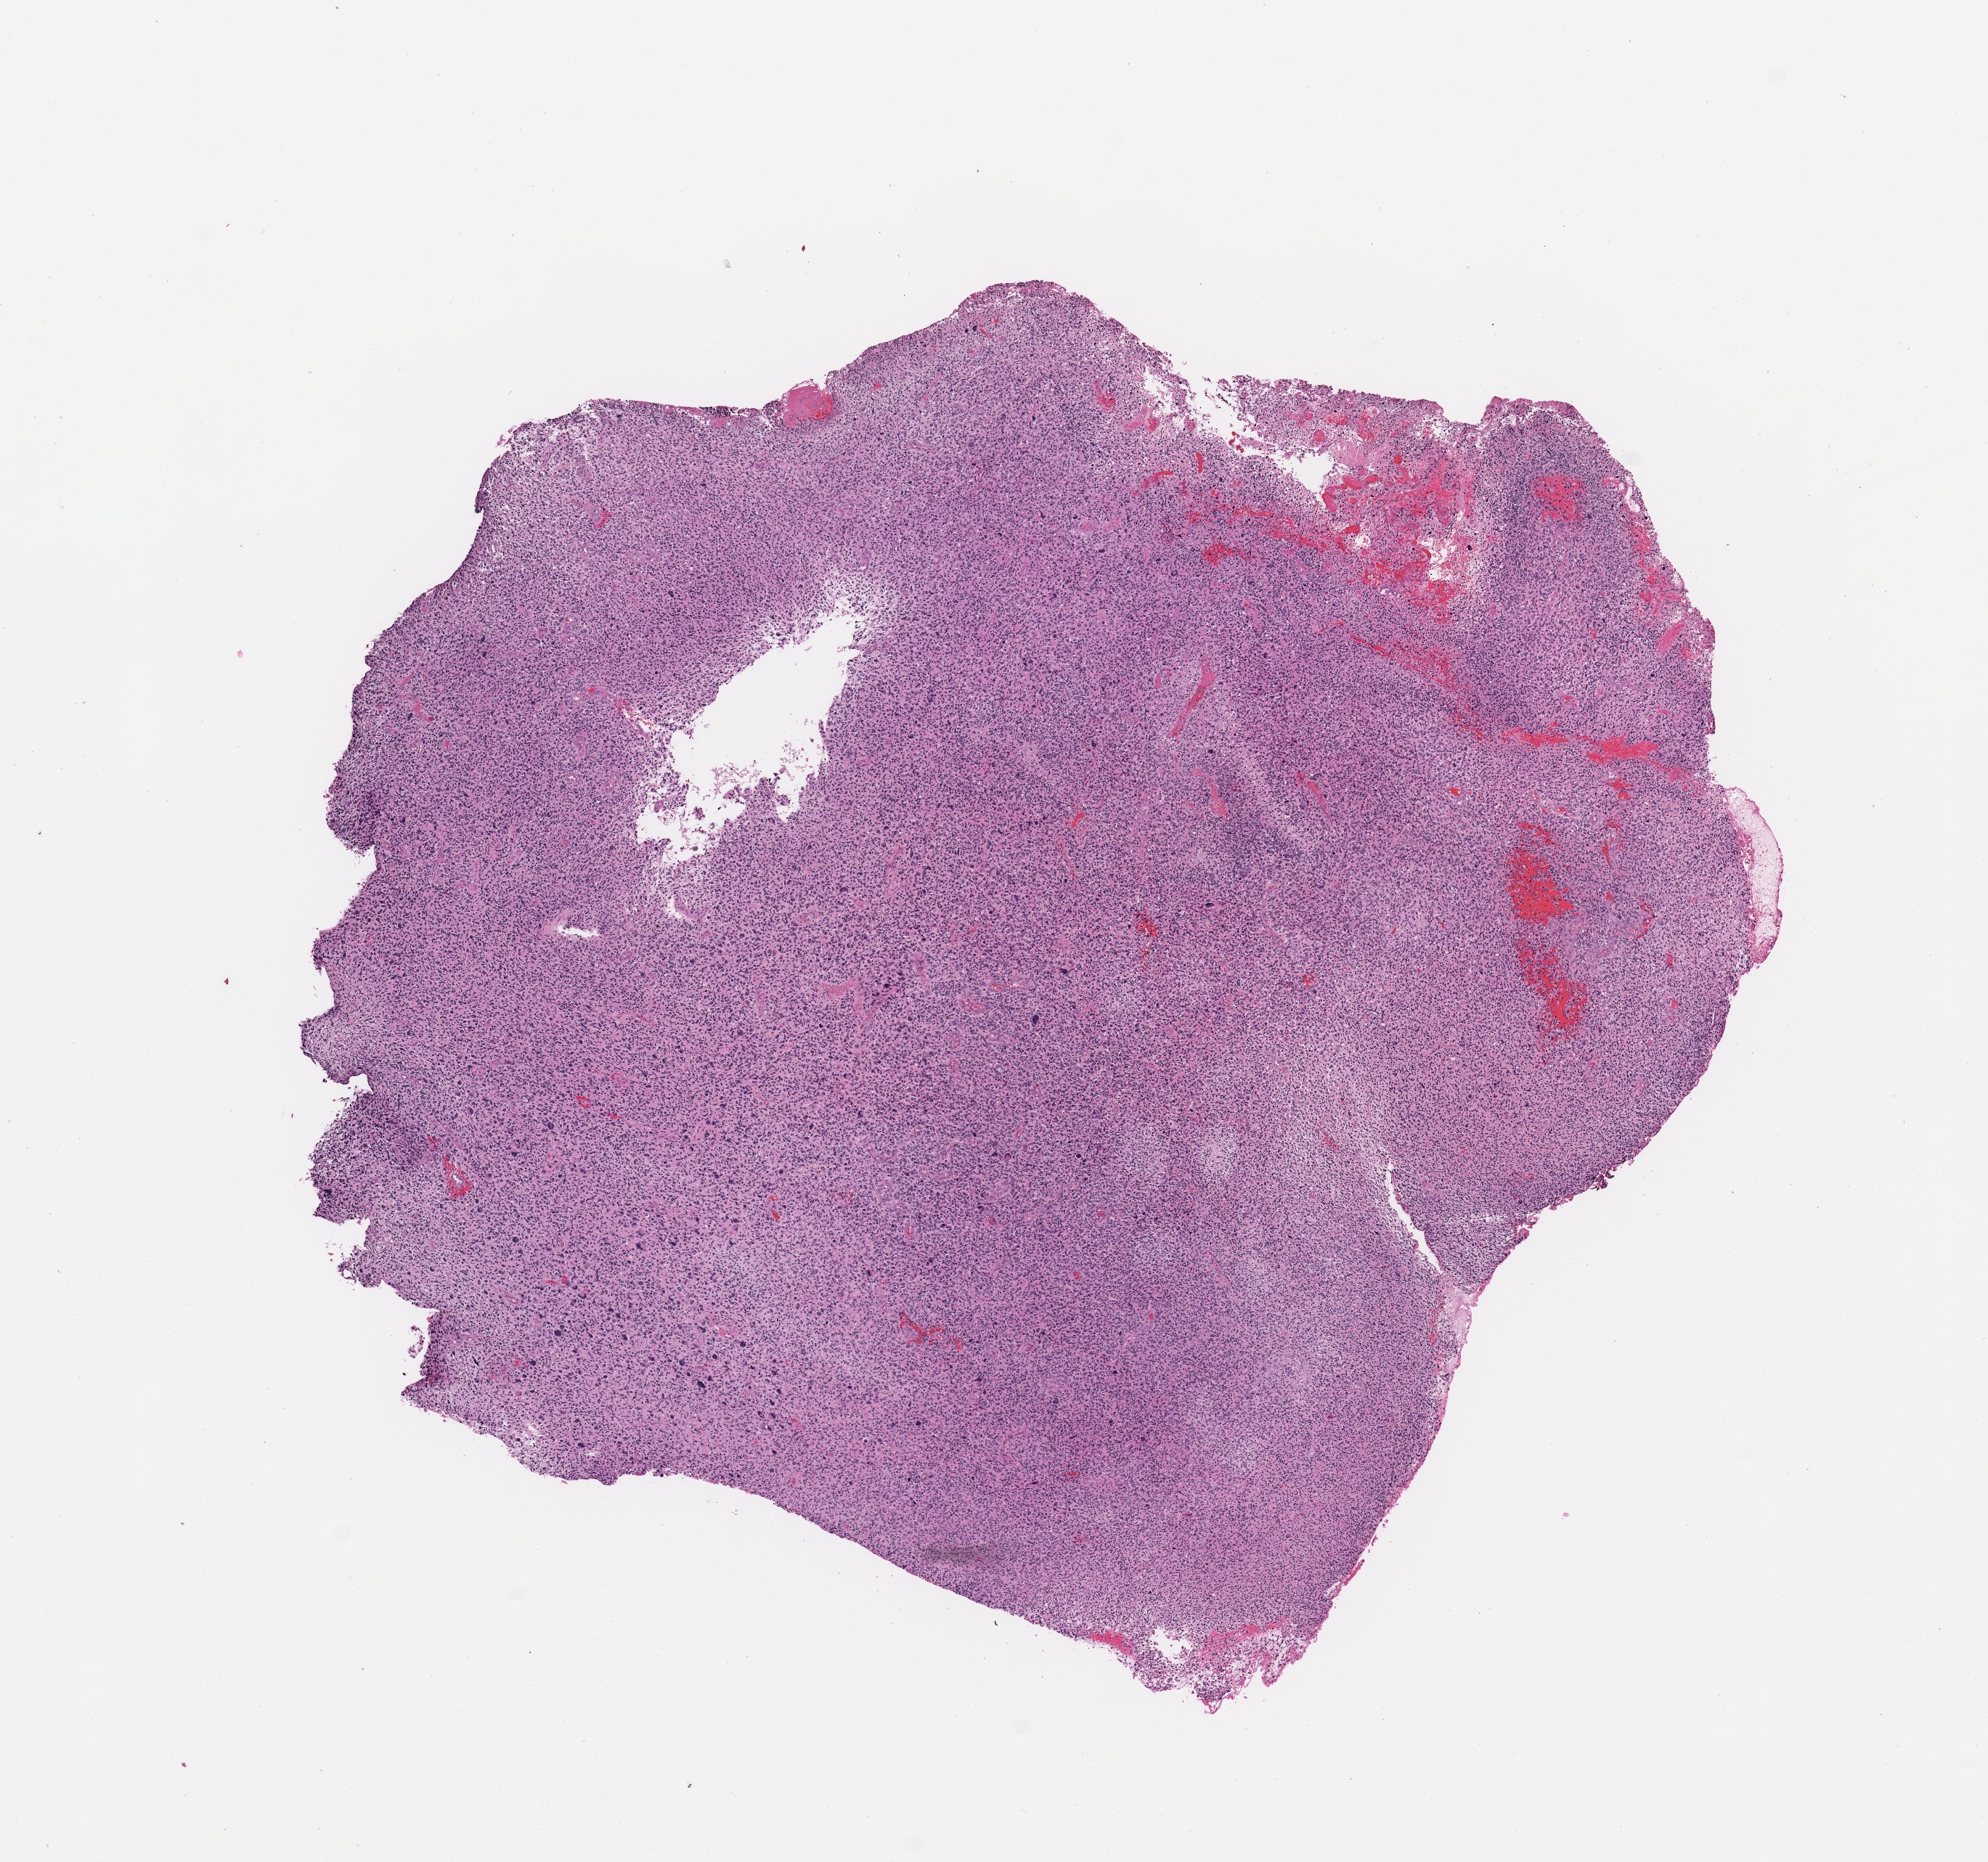
Hematoxylin and eosin (H&E) stained whole-slide image — low-resolution overview of the scanned area, about 10.8 x 10.1 mm (acquisition: 20x scan), tumour tissue sample, sampled site: temporal cortex. Patient: male, age 60 years. Composition of this section per pathologist review: tumour nuclei 80%, necrosis 5%.
Diagnosis: Glioblastoma.